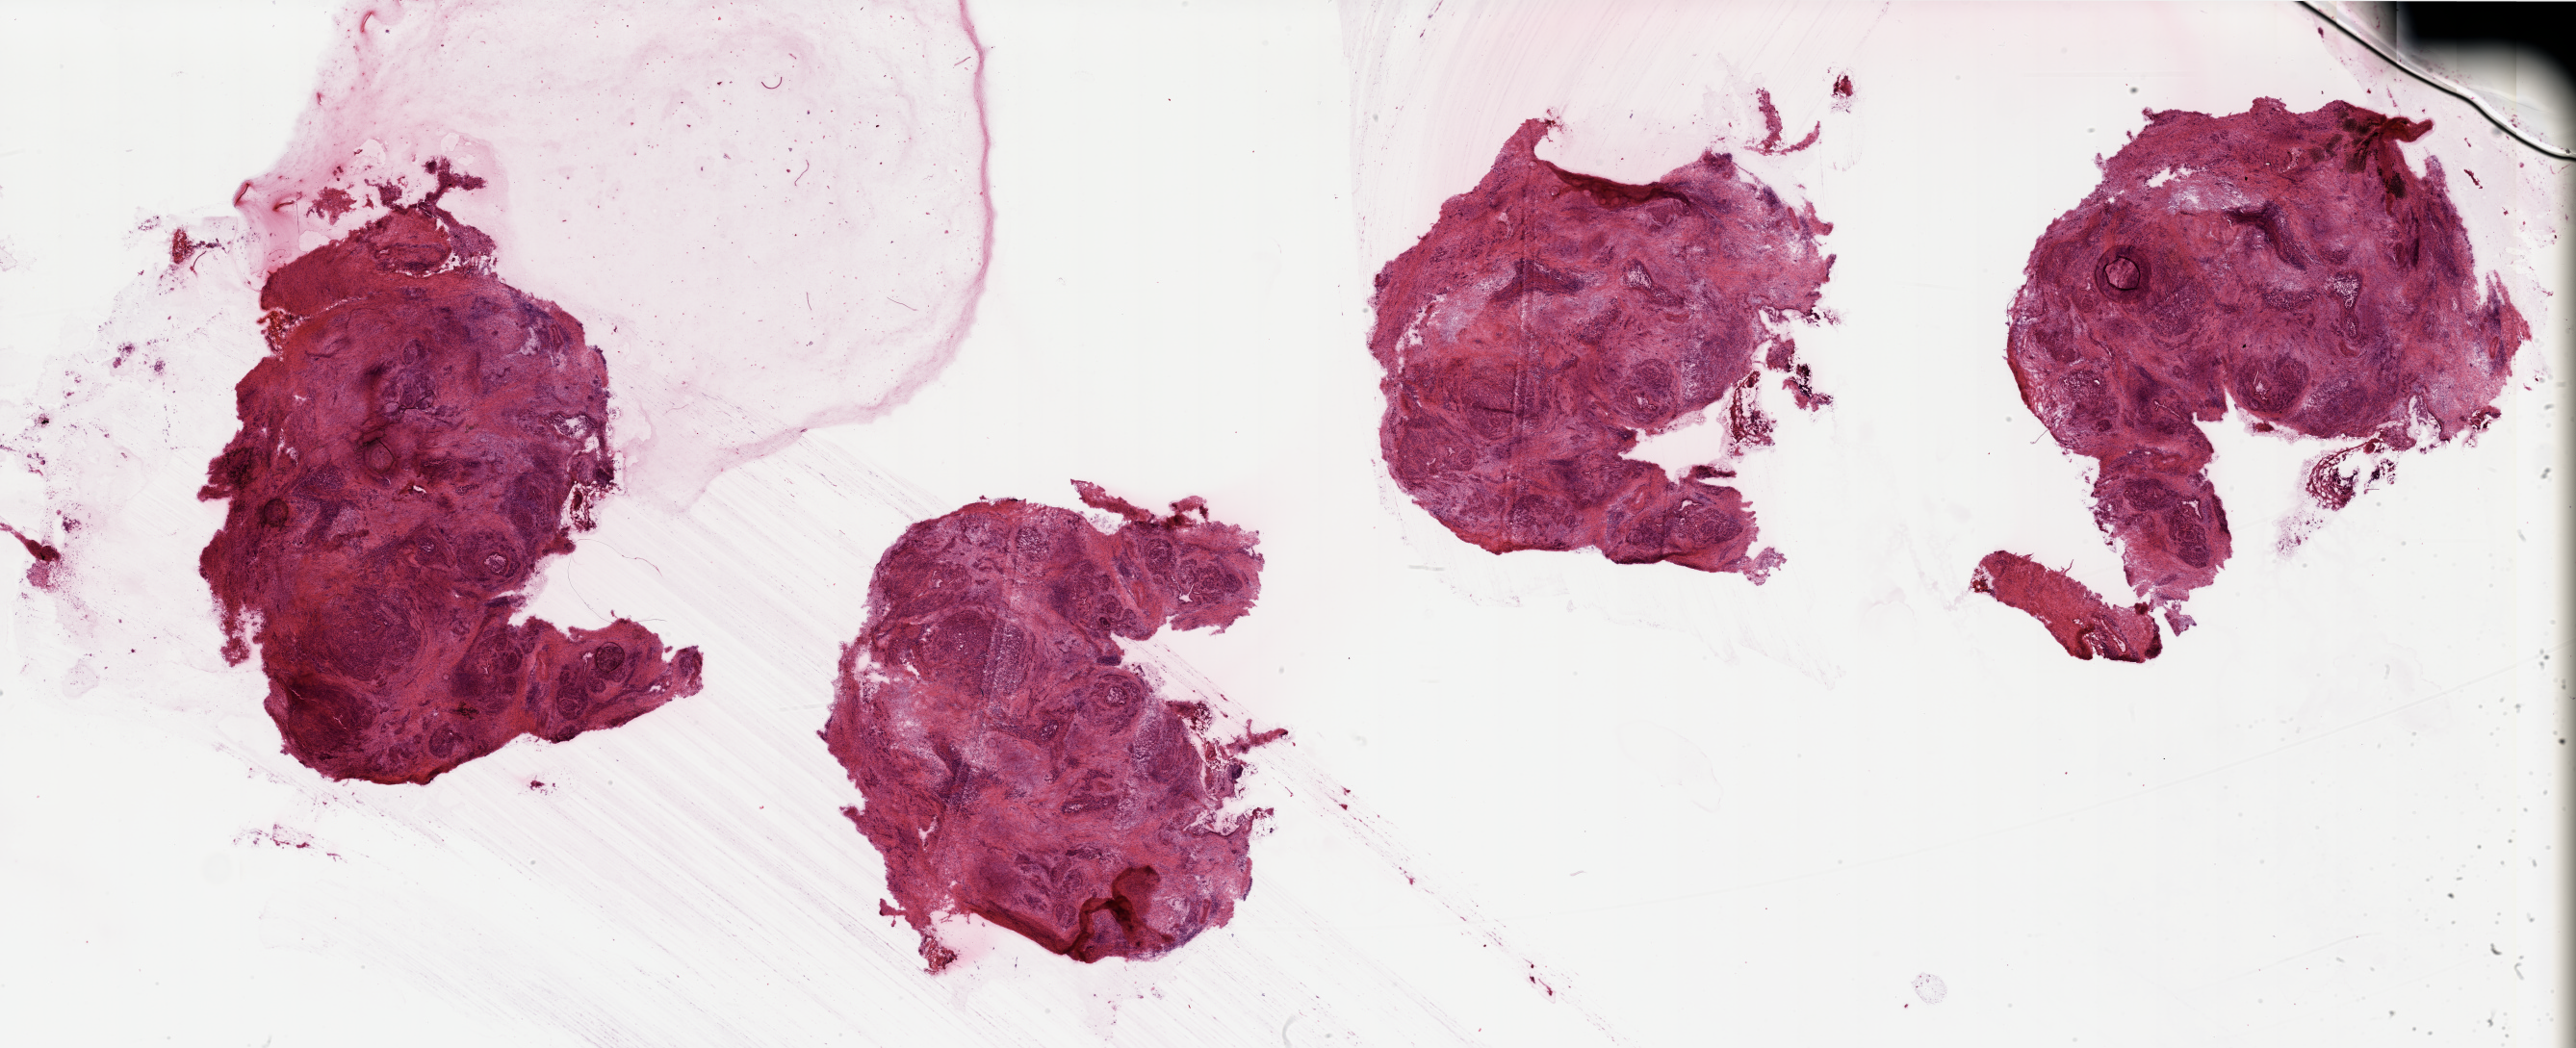
Digitized Hematoxylin and eosin (H&E) stained tissue section (whole slide), shown as a low-resolution overview of the whole scanned area (about 42.3 x 17.2 mm), pancreas, tumour tissue. Male, 58 y/o.
Diagnosis: Infiltrating duct carcinoma, NOS.